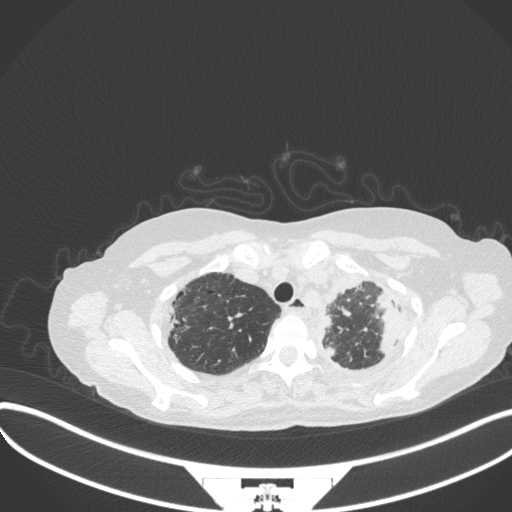
Chest CT, one axial slice; position 288 of 373 along the scan axis; reconstruction kernel B31f; 120 kVp; lung window (W 1500 / L -600 HU); 1 mm slice thickness; 512 × 512 image matrix, field of view 400 × 400 mm. Female patient, age 56 years. From the clinical record (not read from this slice): clinical TNM (as recorded): T1 N0 M0.
Structures marked on this image (rectangle marked by the reading radiologist):
- lung tumour (recorded histology: adenocarcinoma): box from (x=371, y=282) to (x=402, y=365) px